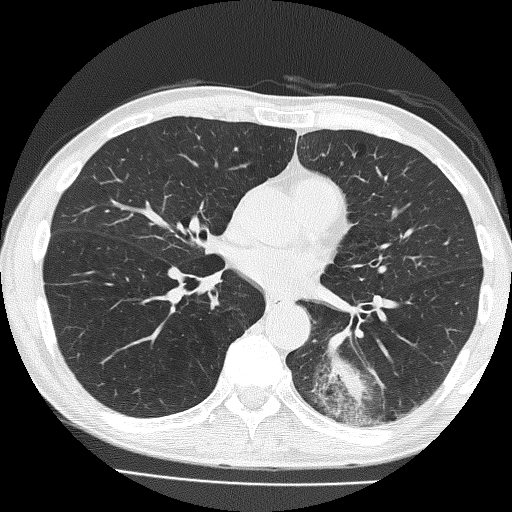
Low-dose screening chest CT, one axial slice. Position 78 of 160 along the scan axis. Reconstruction kernel FC51. 120 kVp. Lung window (W 1500 / L -600 HU). 2 mm slice thickness. 512 × 512 image matrix, field of view 324 × 324 mm.
Outlined on this slice (manually delineated by an expert):
- lesion 1 (tumor, lower lobe of left lung): box from (x=325, y=332) to (x=370, y=405) px